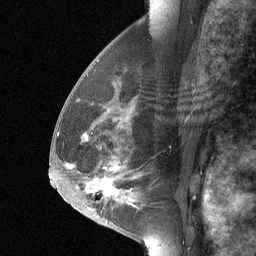
Breast MRI (dynamic contrast-enhanced), one sagittal slice. Dynamic contrast-enhanced study with each time point stored as its own series, time point 2 of 3 at this slice position (early post-contrast, ordered by acquisition time). 1.5 T. TE 4.8 ms, TR 27 ms. 2 mm slice thickness. 256 × 256 image matrix. Patient: female, 56 years. From the clinical record (not read from this slice): setting: breast cancer imaged before/during neoadjuvant chemotherapy; receptor status: HER2-positive.
Annotated regions visible in this slice (semi-automatic segmentation, software-assisted and operator-edited):
- analysis volume of interest (the breast-tissue region the enhancement analysis was run in; not a lesion): box from (x=68, y=83) to (x=142, y=214) px
- tumour enhancement mask (voxels above the 90 % enhancement threshold inside the analysis volume of interest): (x=86, y=165)–(x=119, y=195)